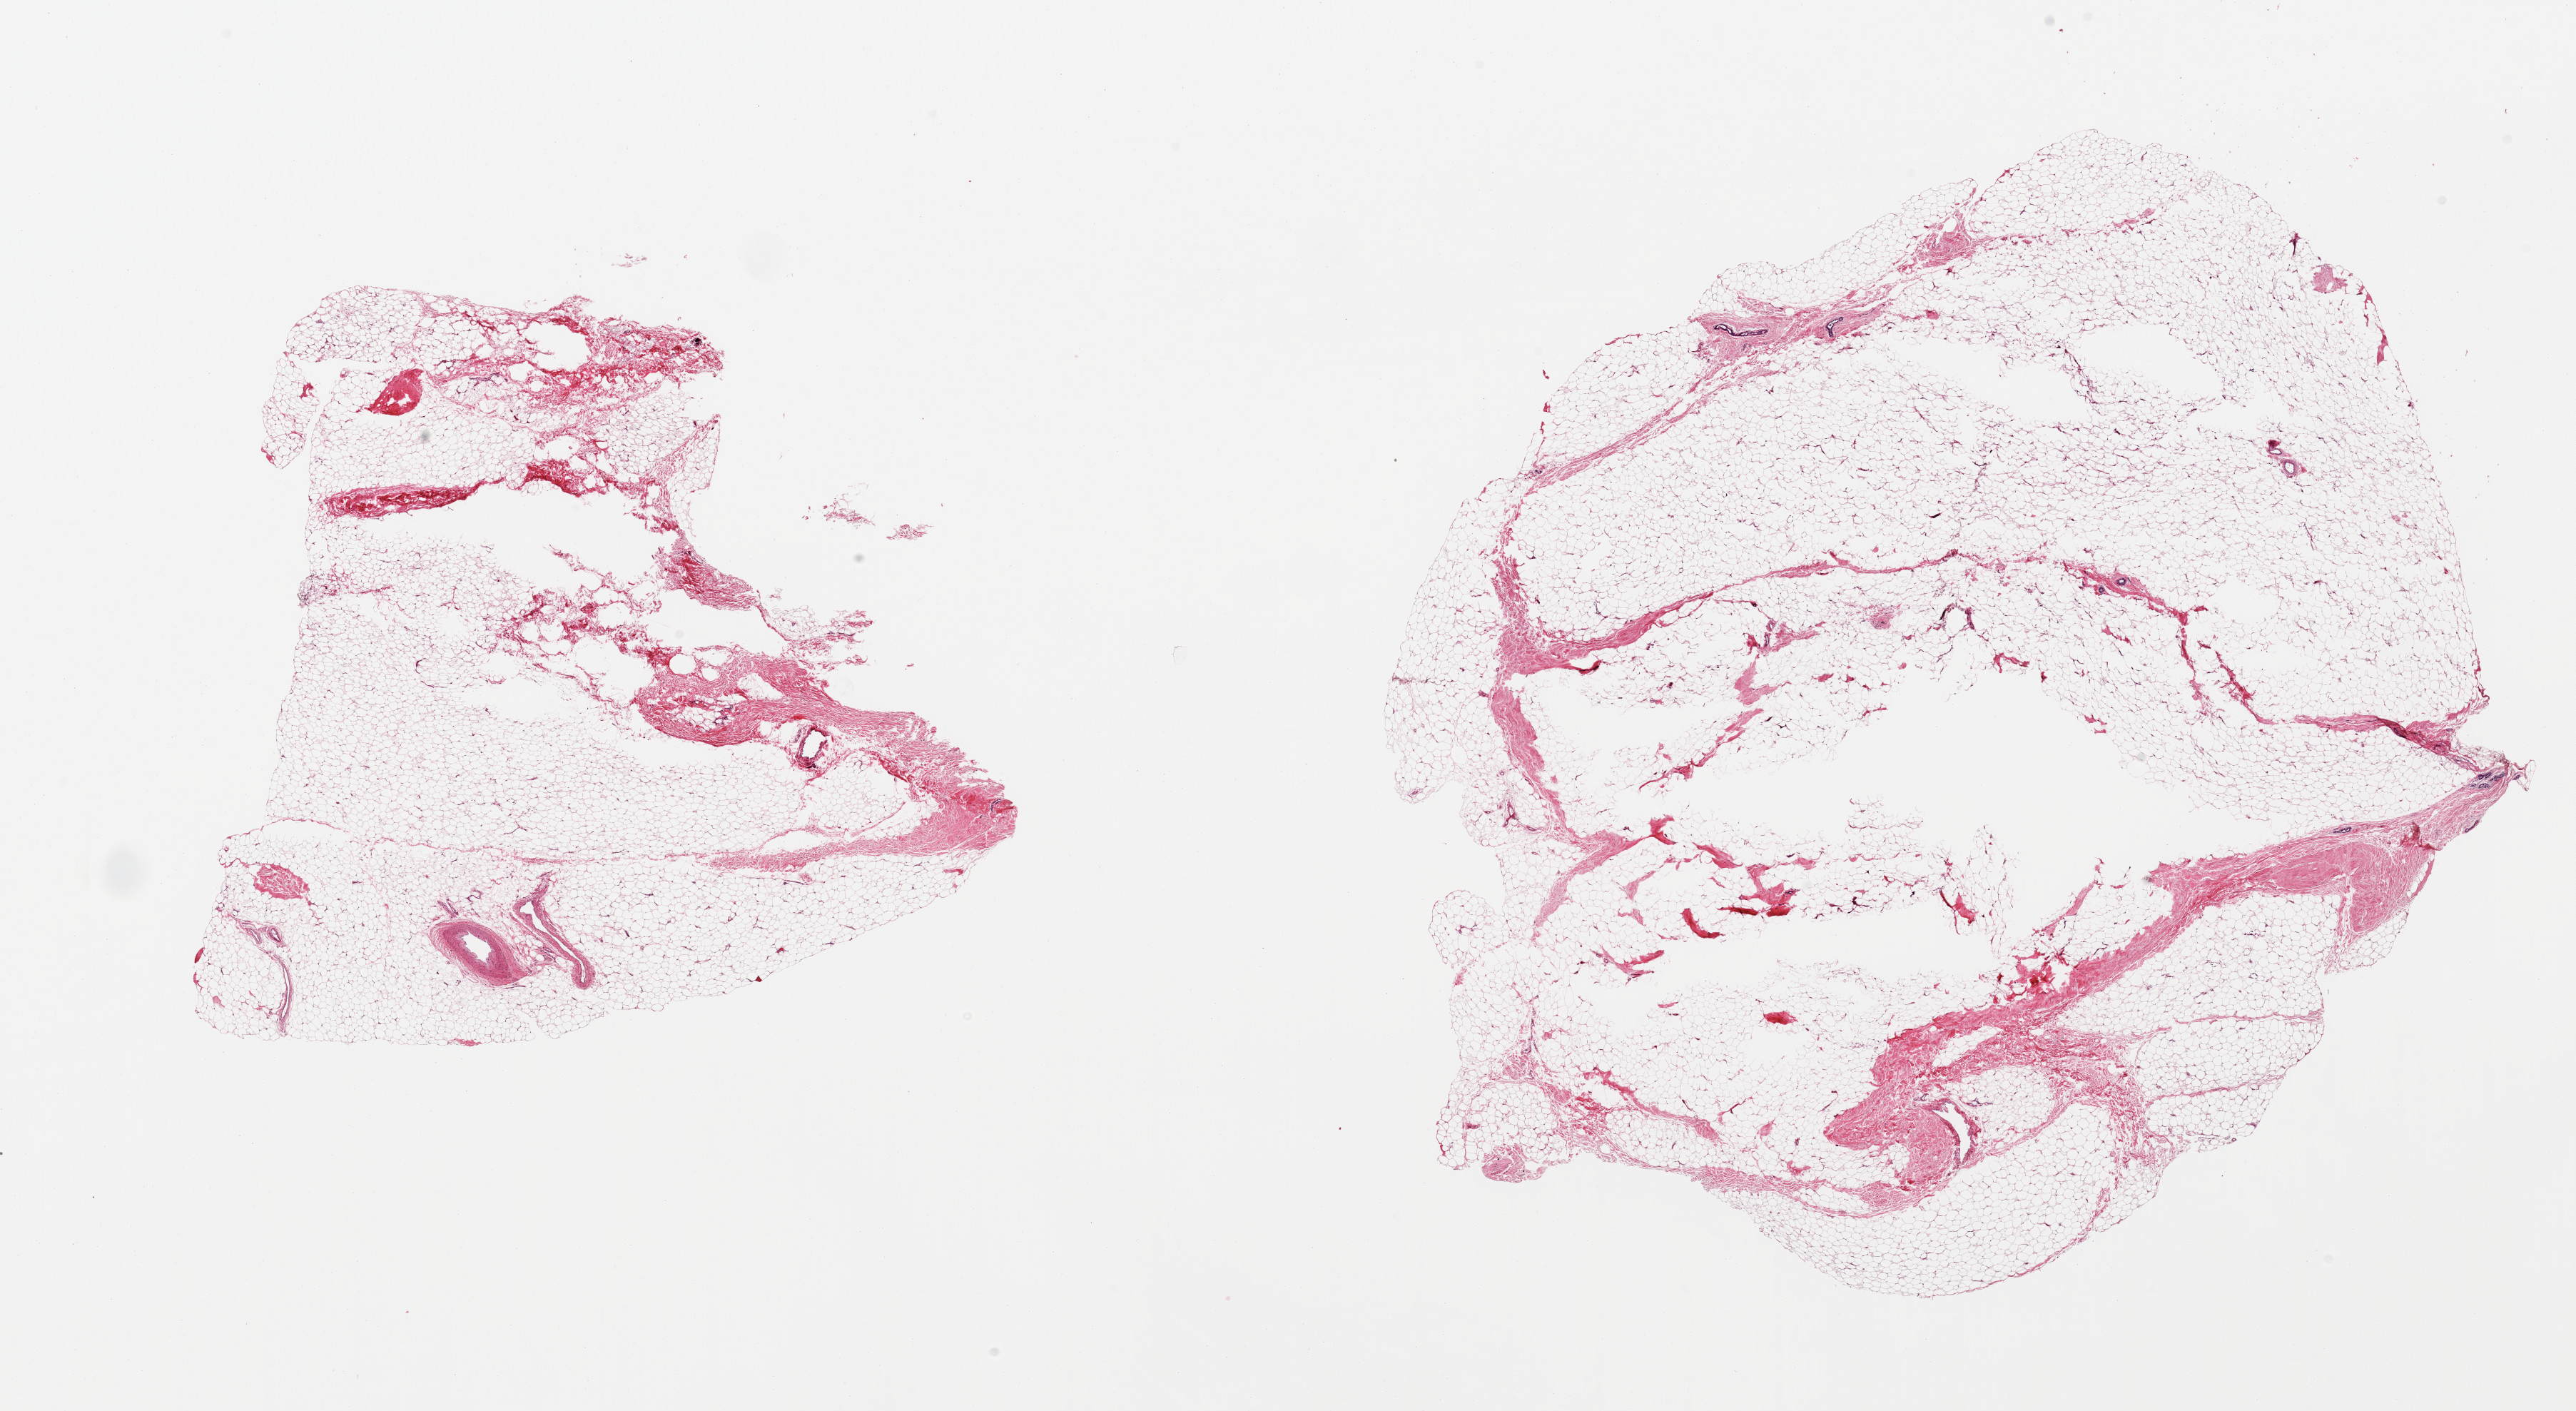
Whole-slide image, H&E stain, brightfield, a low-resolution overview of the entire scanned area, about 28.5 x 15.6 mm (from a 20x scan). PAXgene-fixed paraffin-embedded (PFPE) section. Sampled site (target tissue): breast. Tissue donor sample. Female donor.
Pathologist's review note for this sample: 2 pieces, fibroadipose elements, rare ductal elements.